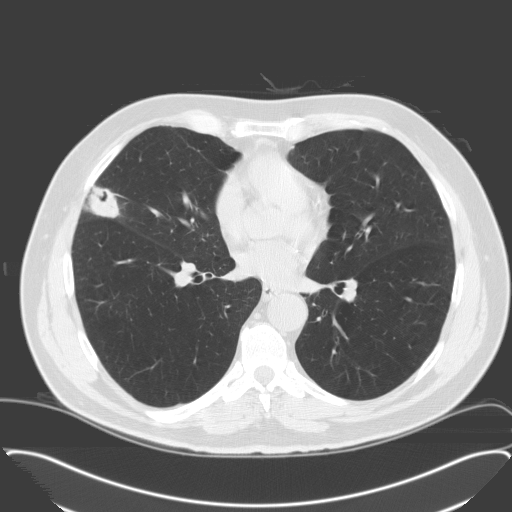
Low-dose screening chest CT, axial slice; third annual screen; lung window (W 1500 / L -600 HU); slice 89 of 174 in the series. Male, age 65 years at enrolment. Former smoker at enrolment.
• Expert-annotated lung lesion, bounding box [x1, y1, x2, y2] px = [67, 173, 131, 230].
• The exam's reader record, not a measurement of the box and not confirmed to be the same lesion: non-calcified nodule or mass ≥4 mm, right middle lobe, 28 × 23 mm, spiculated (stellate) margins, soft tissue attenuation, pre-existing on the prior screen: no.
• Official screen result: positive, other.
• Lung cancer was diagnosed 25 days after this screen: adenocarcinoma, NOS, right middle lobe, moderately differentiated (G2), stage IA (AJCC 6th edition), 25 mm at pathology.